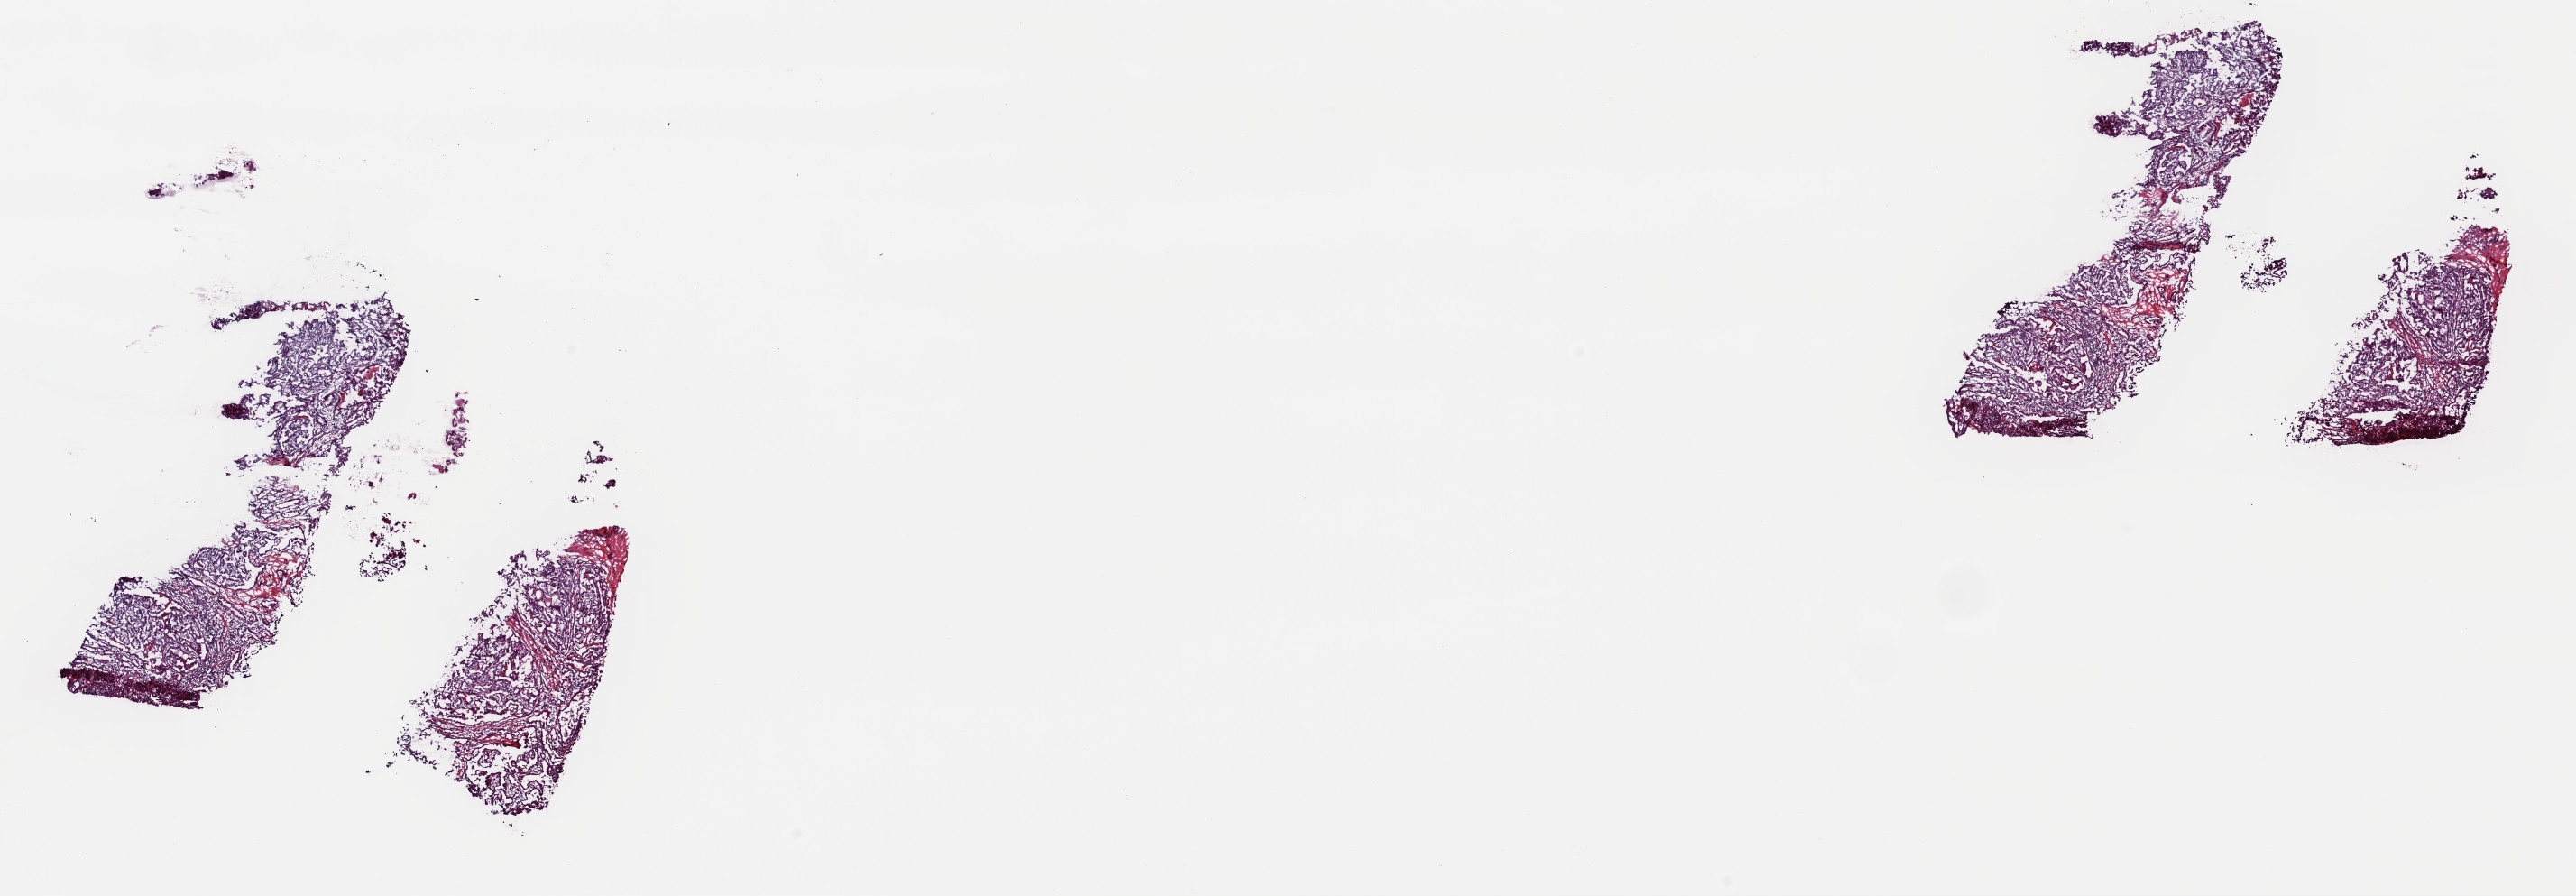
H&E-stained whole-slide image, whole scanned area (about 22.6 x 7.8 mm, slide scanned at 40x) shown as a low-resolution overview; frozen section from the top of the tissue portion; sample: primary tumour, thyroid. Female, age 32 years at initial diagnosis. Pathologist review of this section (percent, as recorded): tumour cells 100%, tumour nuclei 90%, normal cells 0%, stromal cells 0%, necrosis 0%. Inflammatory infiltration, as recorded: lymphocyte infiltration 0%, monocyte infiltration 0%, neutrophil infiltration 0%.
AJCC pathologic stage: I (6th edition). Pathologic diagnosis: Papillary adenocarcinoma, NOS (thyroid gland). Lymph nodes positive (case pathology): 3 of 12 examined.